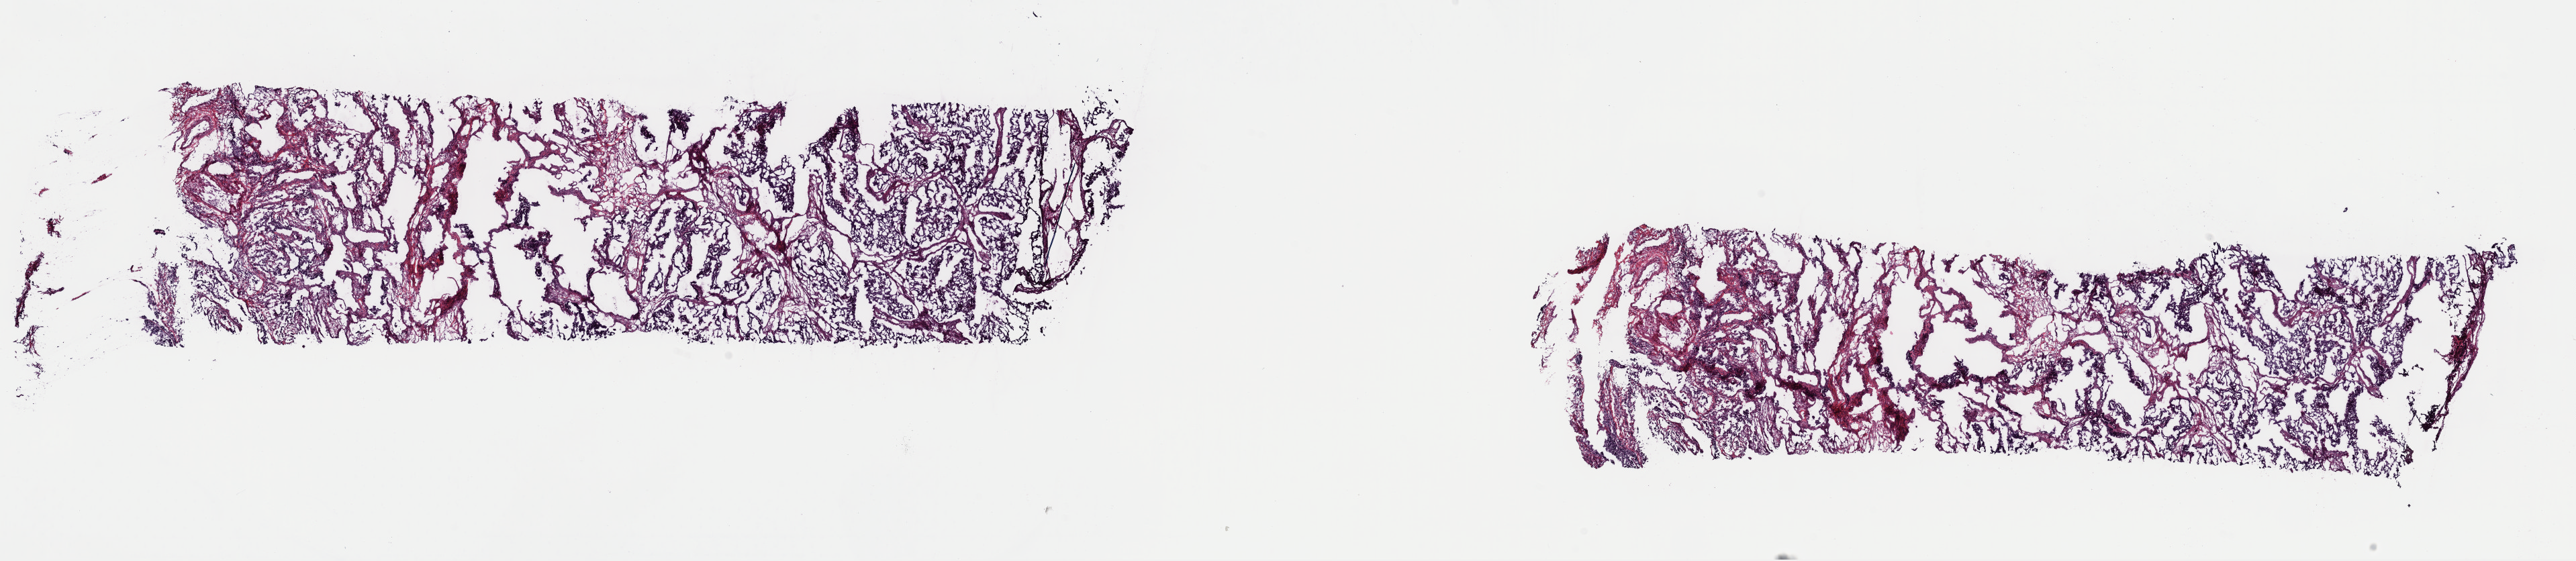
H&E-stained whole-slide image — low-resolution overview of the scanned area, about 30.3 x 6.6 mm (acquisition: 40x scan), frozen section from the top of the tissue portion, sample: primary tumour, cervix. Female patient; age at initial diagnosis 49 years. Histologic grade: G2 (moderately differentiated). Composition of this section per pathologist review: tumour cells 55%, tumour nuclei 60%, normal cells 0%, stromal cells 40%, necrosis 5%. Infiltration values recorded for this section: lymphocyte infiltration 5%, monocyte infiltration 3%, neutrophil infiltration 3%.
Diagnosis: Adenocarcinoma, endocervical type (cervix uteri). FIGO stage: IB2.